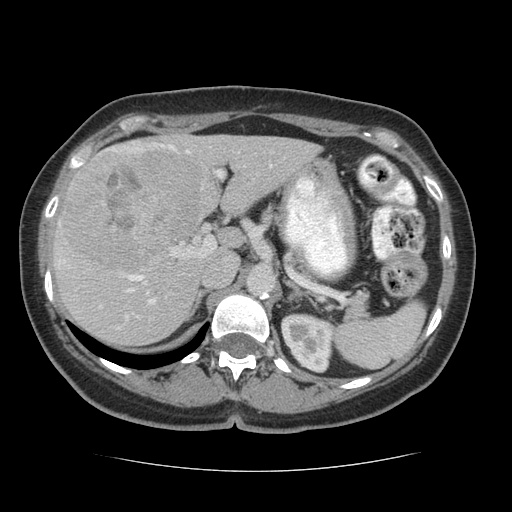
Contrast-enhanced abdominal CT (liver protocol), one axial slice; position 39 of 75 along the scan axis; 140 kVp; soft-tissue window (W 400 / L 40 HU); 512 × 512 image matrix, field of view 360 × 360 mm. From the clinical record (not read from this slice): diagnosis: hepatocellular carcinoma (patient treated with transarterial chemoembolisation; whether this scan precedes or follows treatment is not stated here); TNM stage (as recorded): Stage-I; Child-Pugh class: A; tumour differentiation: moderately differentiated; tumour nodularity: uninodular.
Annotated regions visible in this slice (semi-automatic segmentation, software-assisted and operator-edited):
- liver parenchyma outside the tumour (the mass and vessels are separate outlines, so this box may not span the whole liver): bounding box (x1, y1, x2, y2) in pixels: (52, 132, 318, 345)
- mass: (62, 147, 200, 273)
- liver vessels: (58, 142, 272, 329)